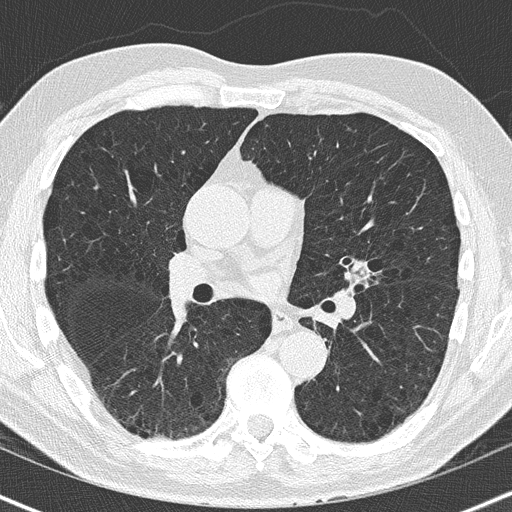
Low-dose screening chest CT, axial slice; baseline annual screen; lung window (W 1500 / L -600 HU); 120 kVp; slice 80 of 163 in the series. Male, age 63 years at enrolment.
Lesion marked by an expert reader, bounding box <336,255,384,295> (left, top, right, bottom; pixels). The screening reader recorded 2 non-calcified nodules or masses ≥4 mm on this exam; which of them this box marks is not recorded. Official screen result: positive, change unspecified: nodule(s) >= 4 mm or enlarging nodule(s), mass(es), or other non-specific abnormalities suspicious for lung cancer. Later outcome: lung cancer diagnosed 32 days after this screen — squamous cell carcinoma, NOS, left upper lobe, moderately differentiated (G2), stage IA (AJCC 6th edition), 23 mm at pathology.